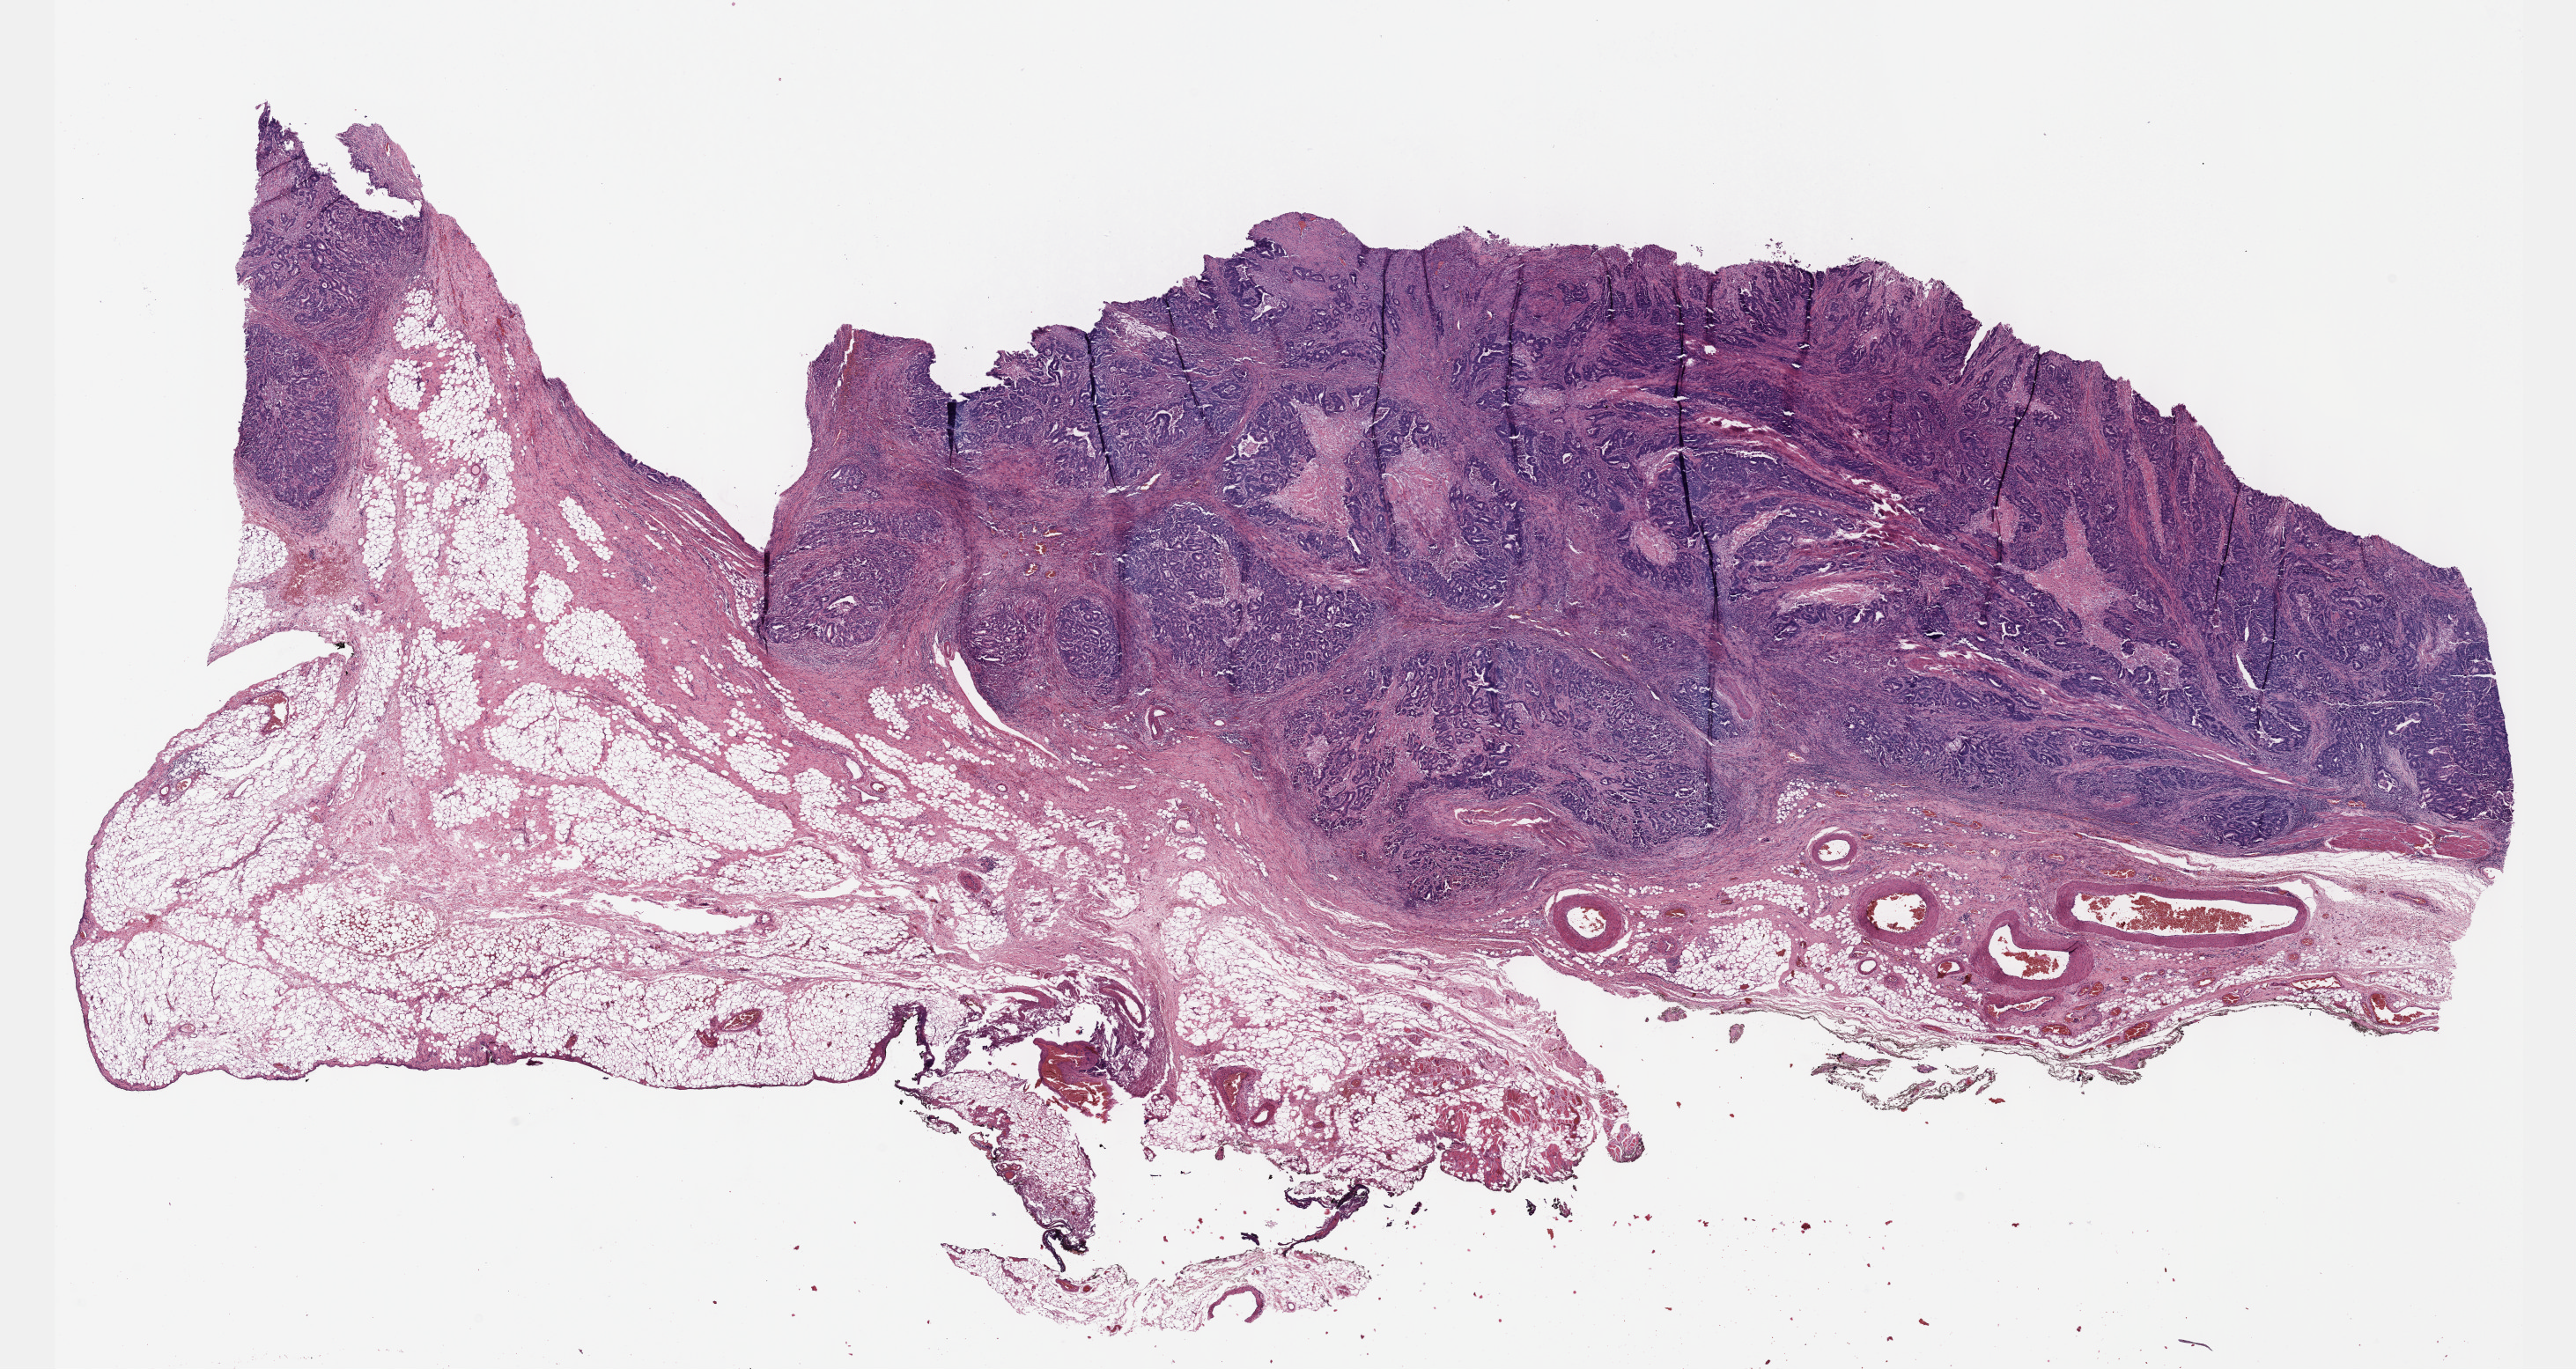
Digitized H&E-stained tissue section (whole slide), shown as a low-resolution overview of the whole scanned area (about 23.6 x 12.6 mm, from a 40x scan). FFPE section. Primary tumour sample from the stomach. Male patient; age at initial diagnosis 78 years. Histologic grade: G2 (moderately differentiated).
Lymph nodes positive (case pathology): 2 of 24 examined. AJCC pathologic stage: IIIA (6th edition). Pathologic diagnosis: Adenocarcinoma, intestinal type (cardia, NOS).